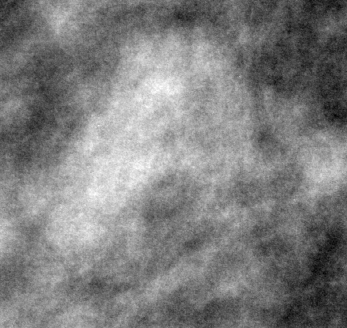
Crop from a digitized film mammogram around one marked abnormality; right breast; MLO view.
Marked abnormality: mass, shape lobulated, margins circumscribed; BI-RADS assessment category 4; pathology result (as recorded, not read from the image): benign.